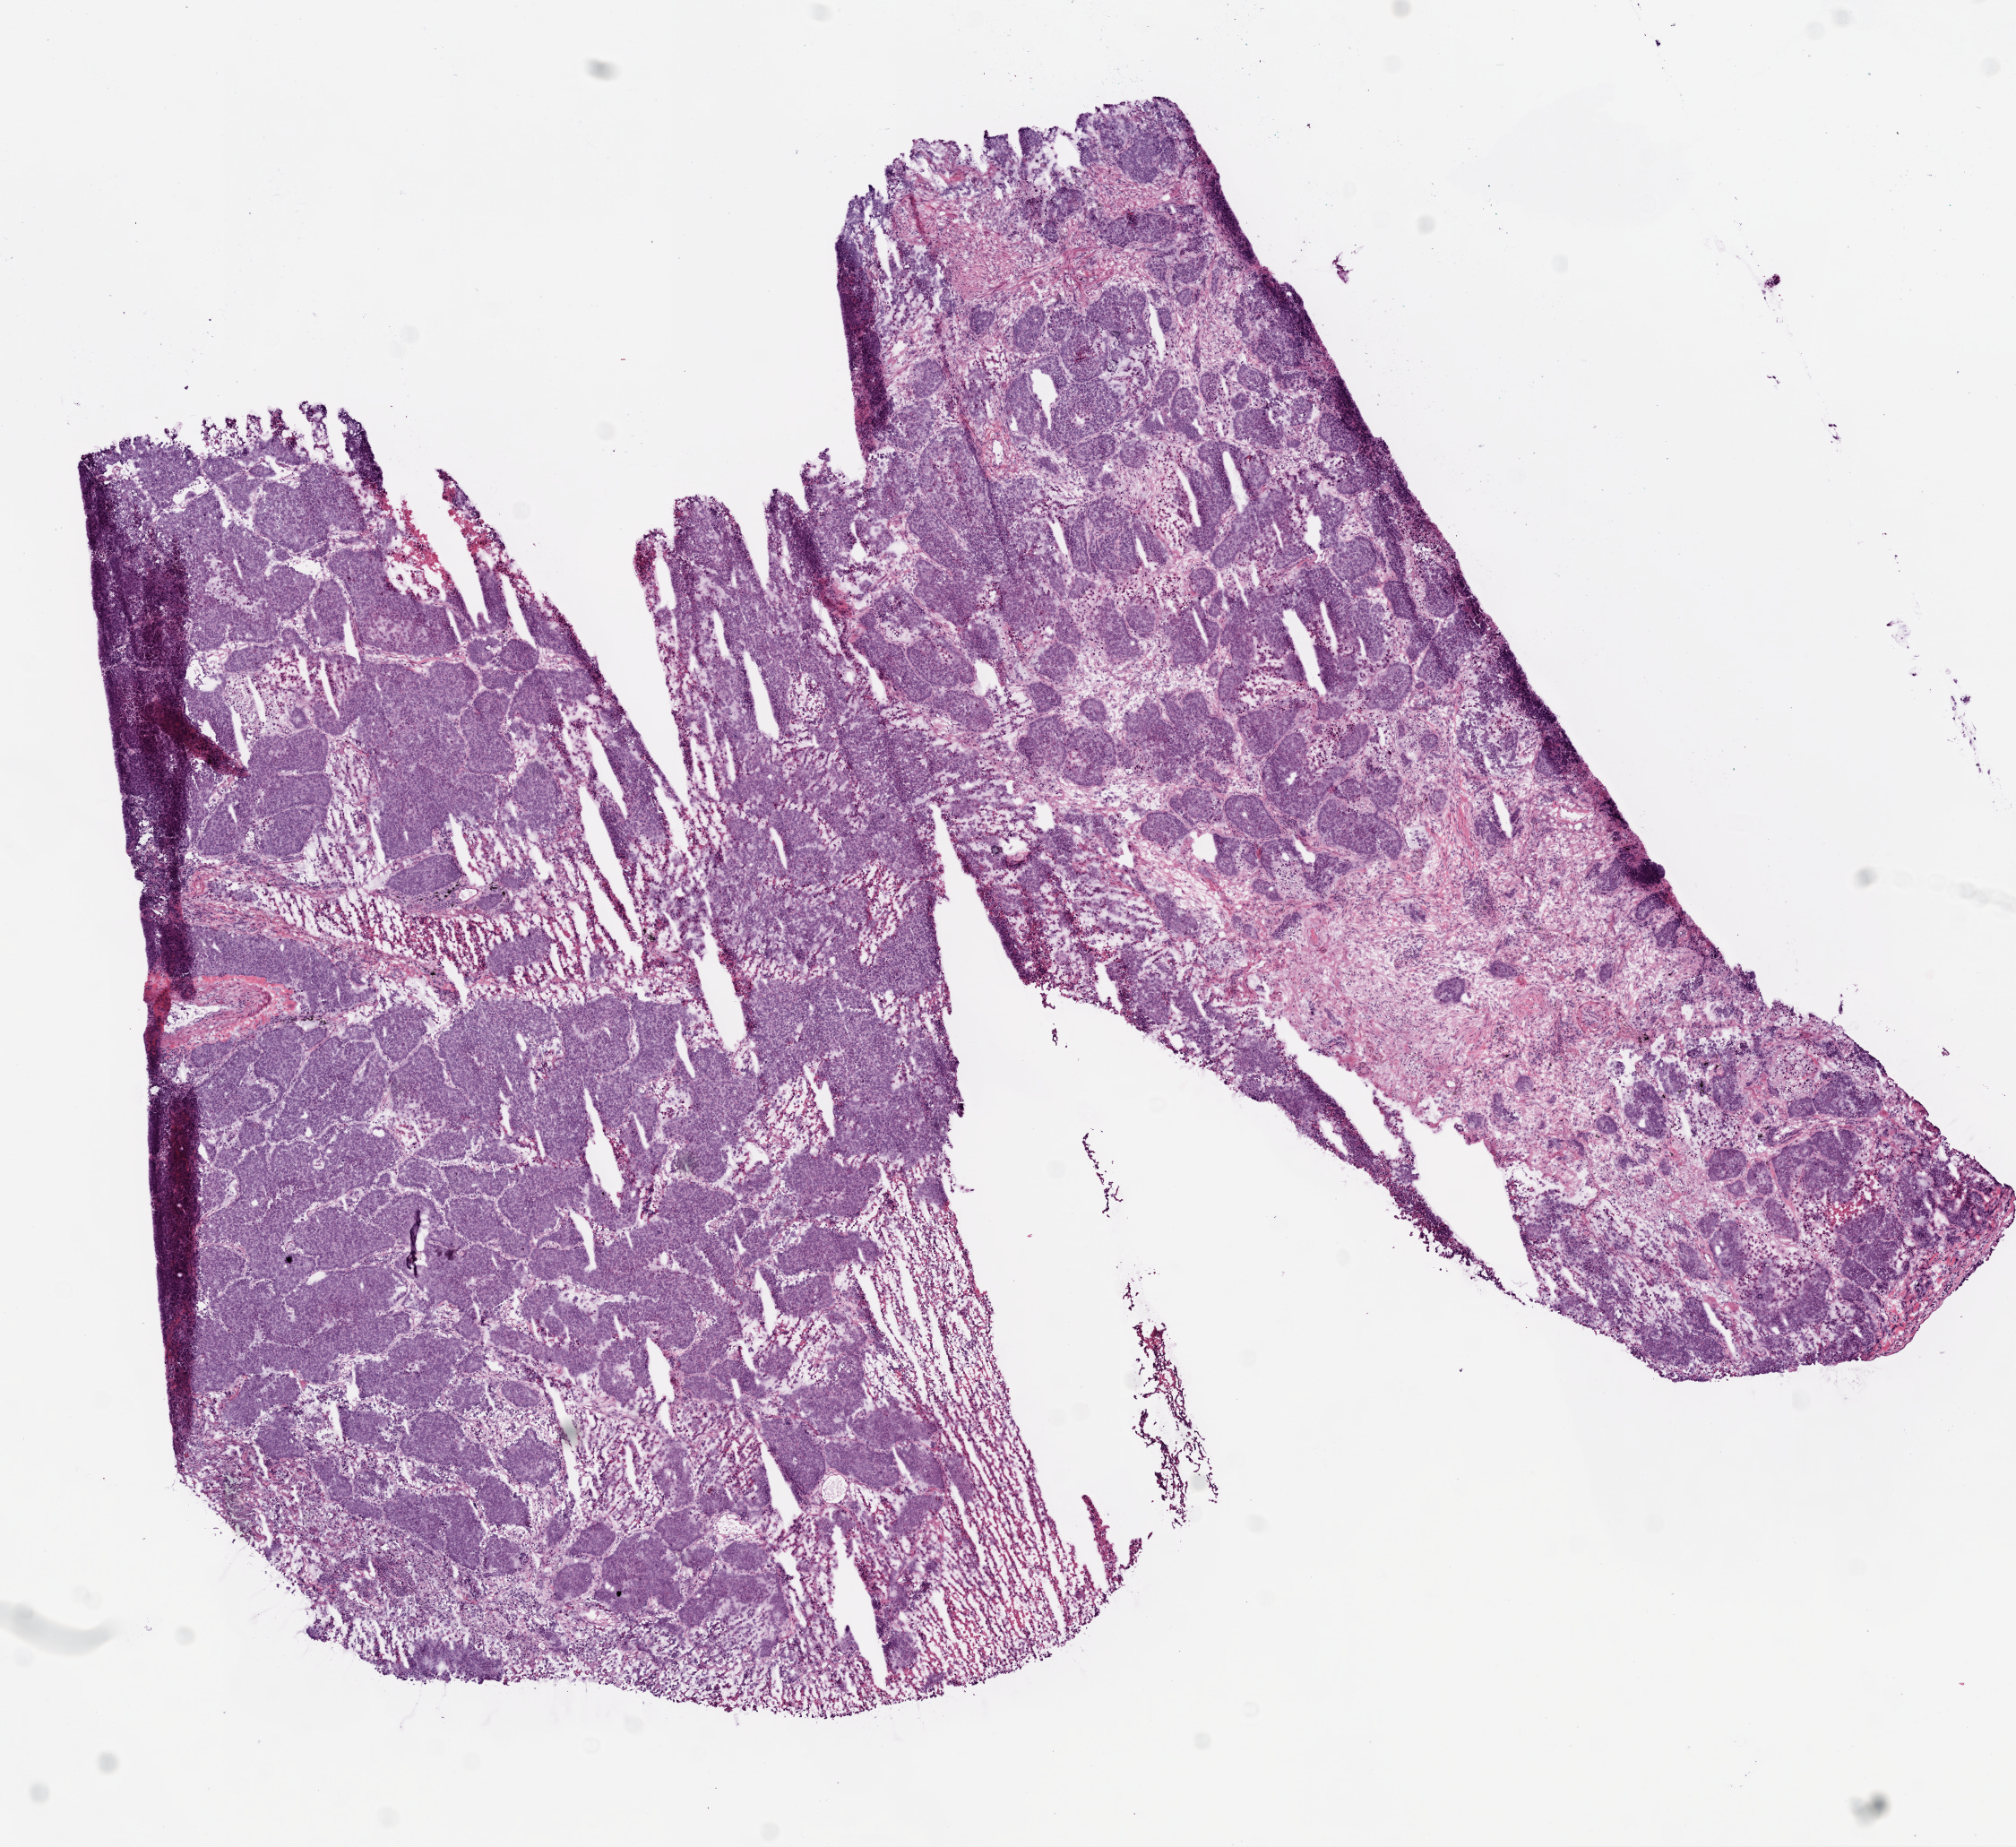
H&E whole-slide image, a low-resolution overview of the entire scanned area, about 9.0 x 8.3 mm, frozen section from the bottom of the tissue portion, lung, primary tumour sample. Patient: male, age at initial diagnosis 66 years. Composition of this section per pathologist review: tumour cells 75%, tumour nuclei 90%, normal cells 0%, stromal cells 5%, necrosis 20%.
AJCC pathologic stage: IIIA (6th edition). Laterality: right. Histologic diagnosis: Squamous cell carcinoma, NOS (upper lobe, lung).